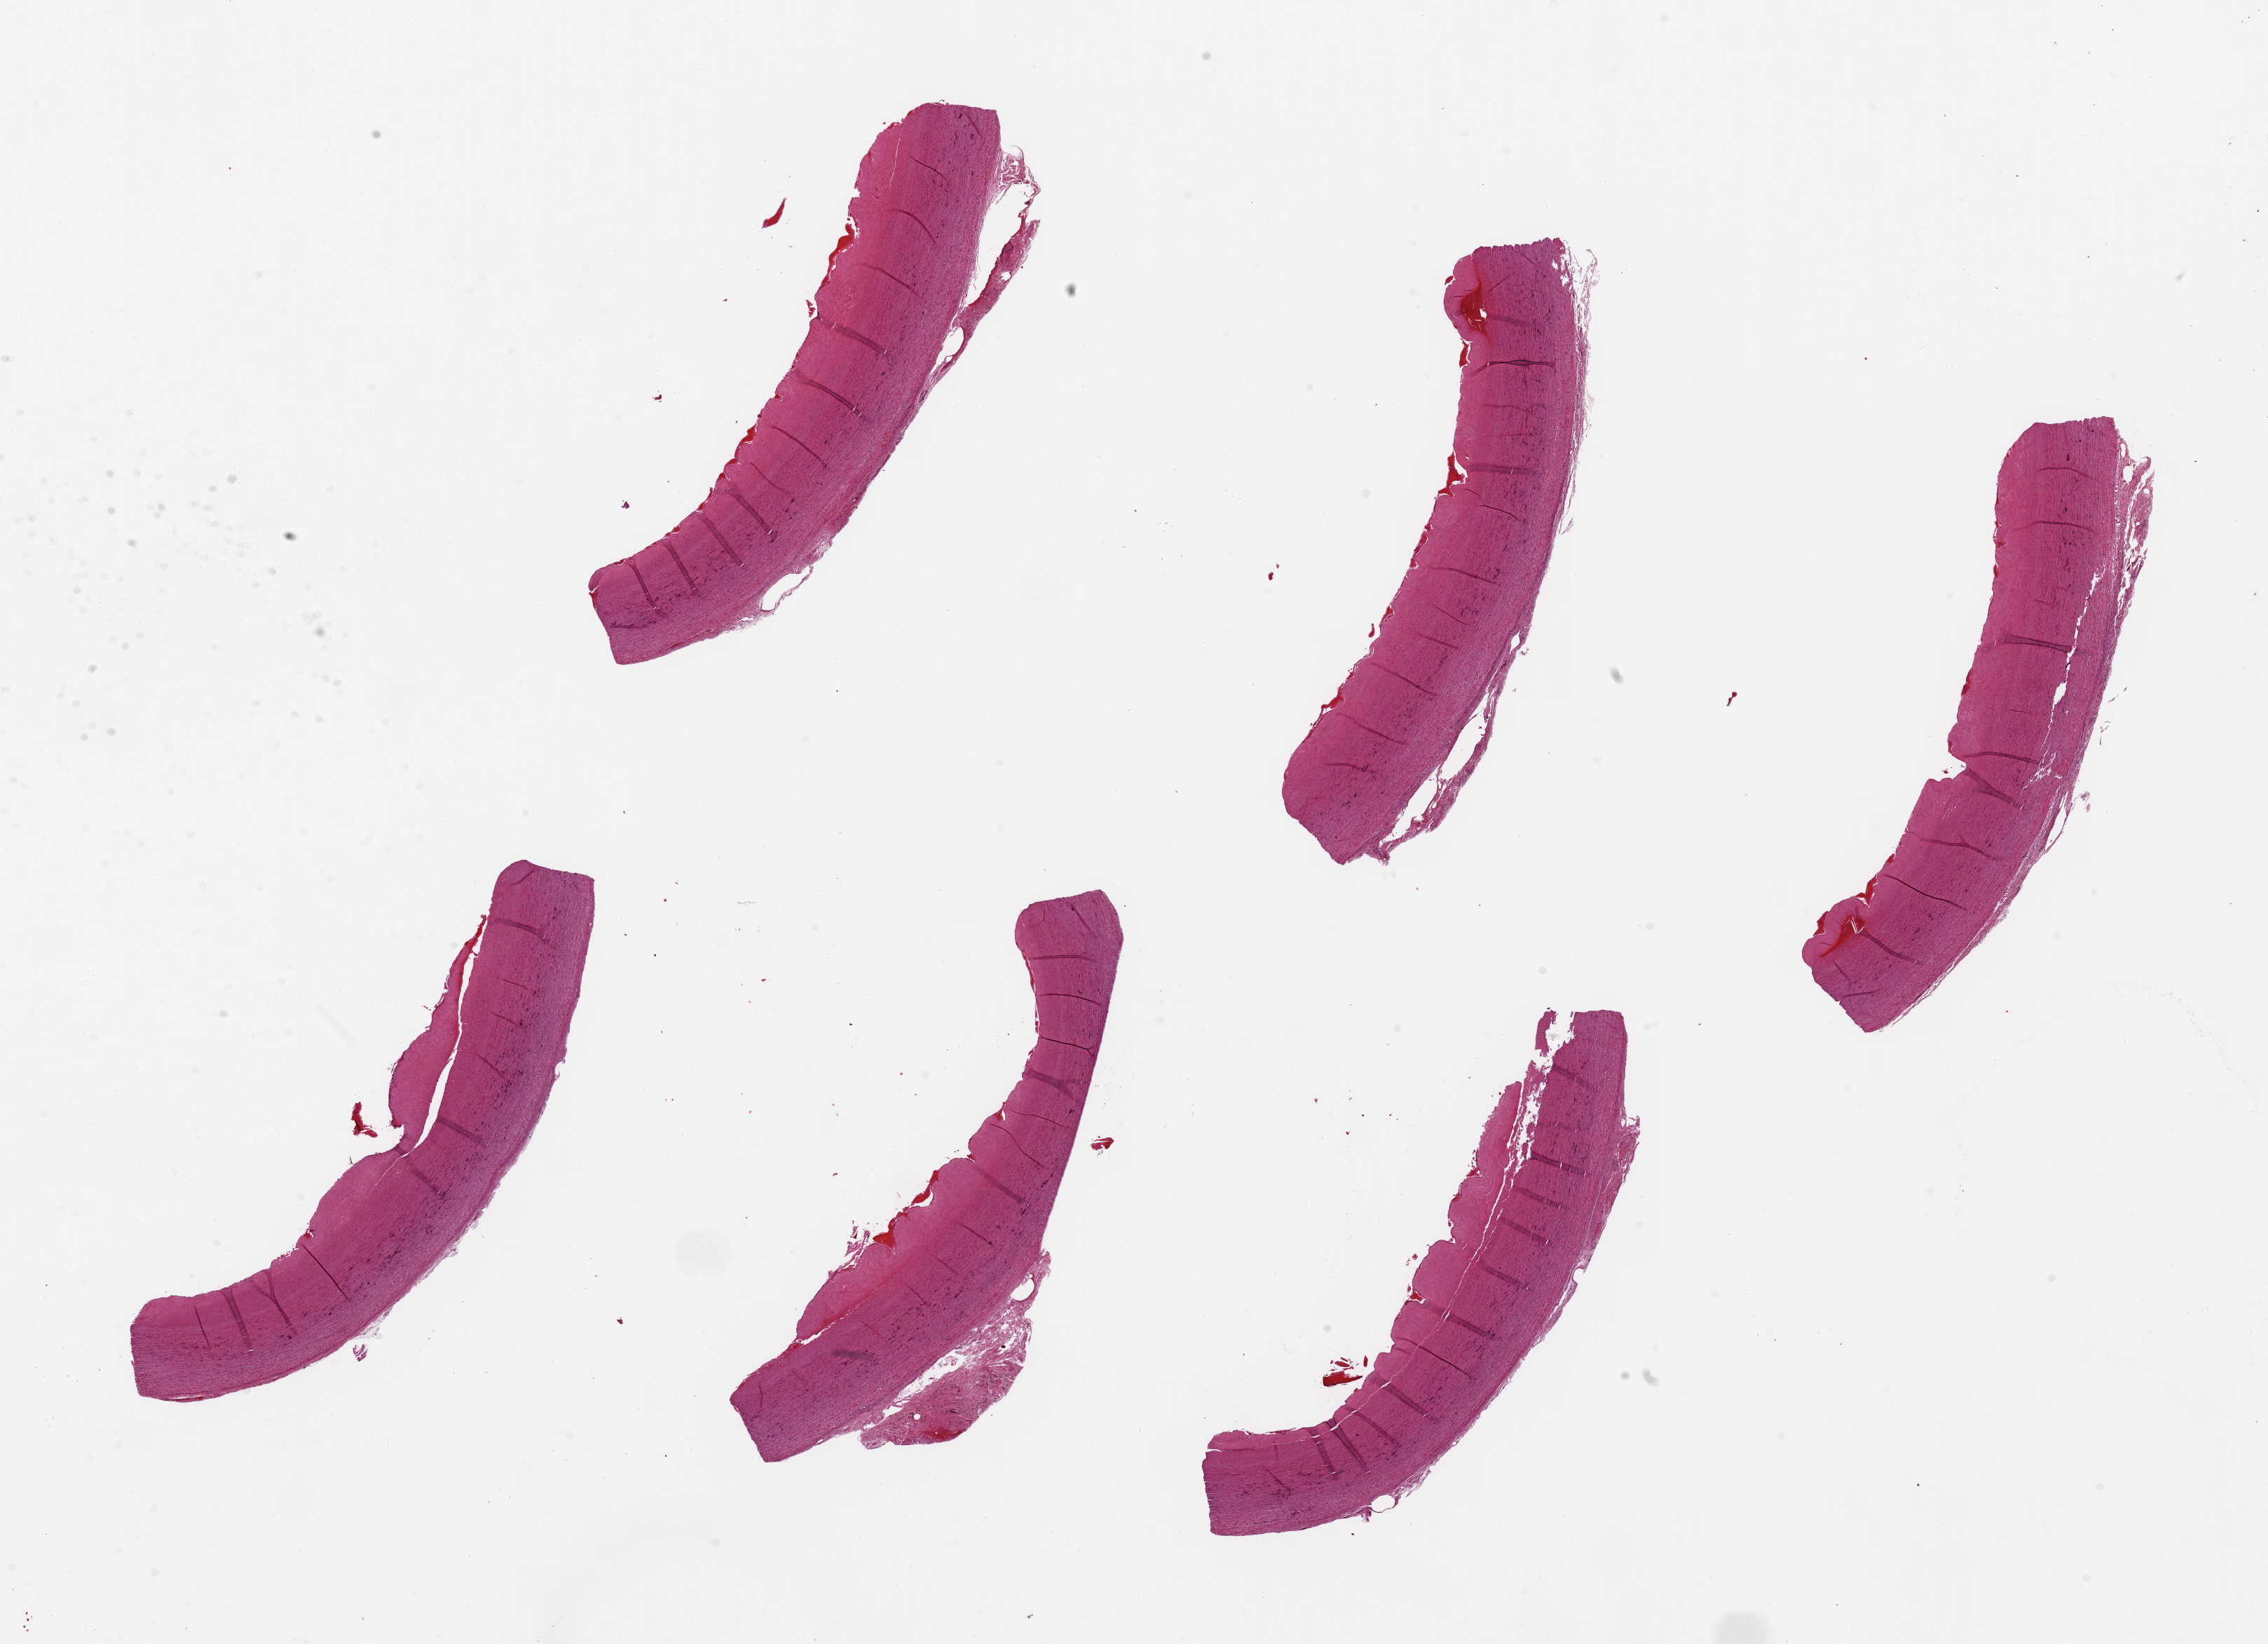
Haematoxylin and eosin whole-slide image — whole scanned area (about 25.6 x 18.6 mm, acquisition: 20x scan) shown as a low-resolution overview, PAXgene-fixed, paraffin-embedded tissue, sampled site (target tissue): aorta, donor tissue sample. Male donor.
* reviewer comment on this tissue sample: 6 pieces ~8x1.5mm, upto 0.5mm atherosis layer